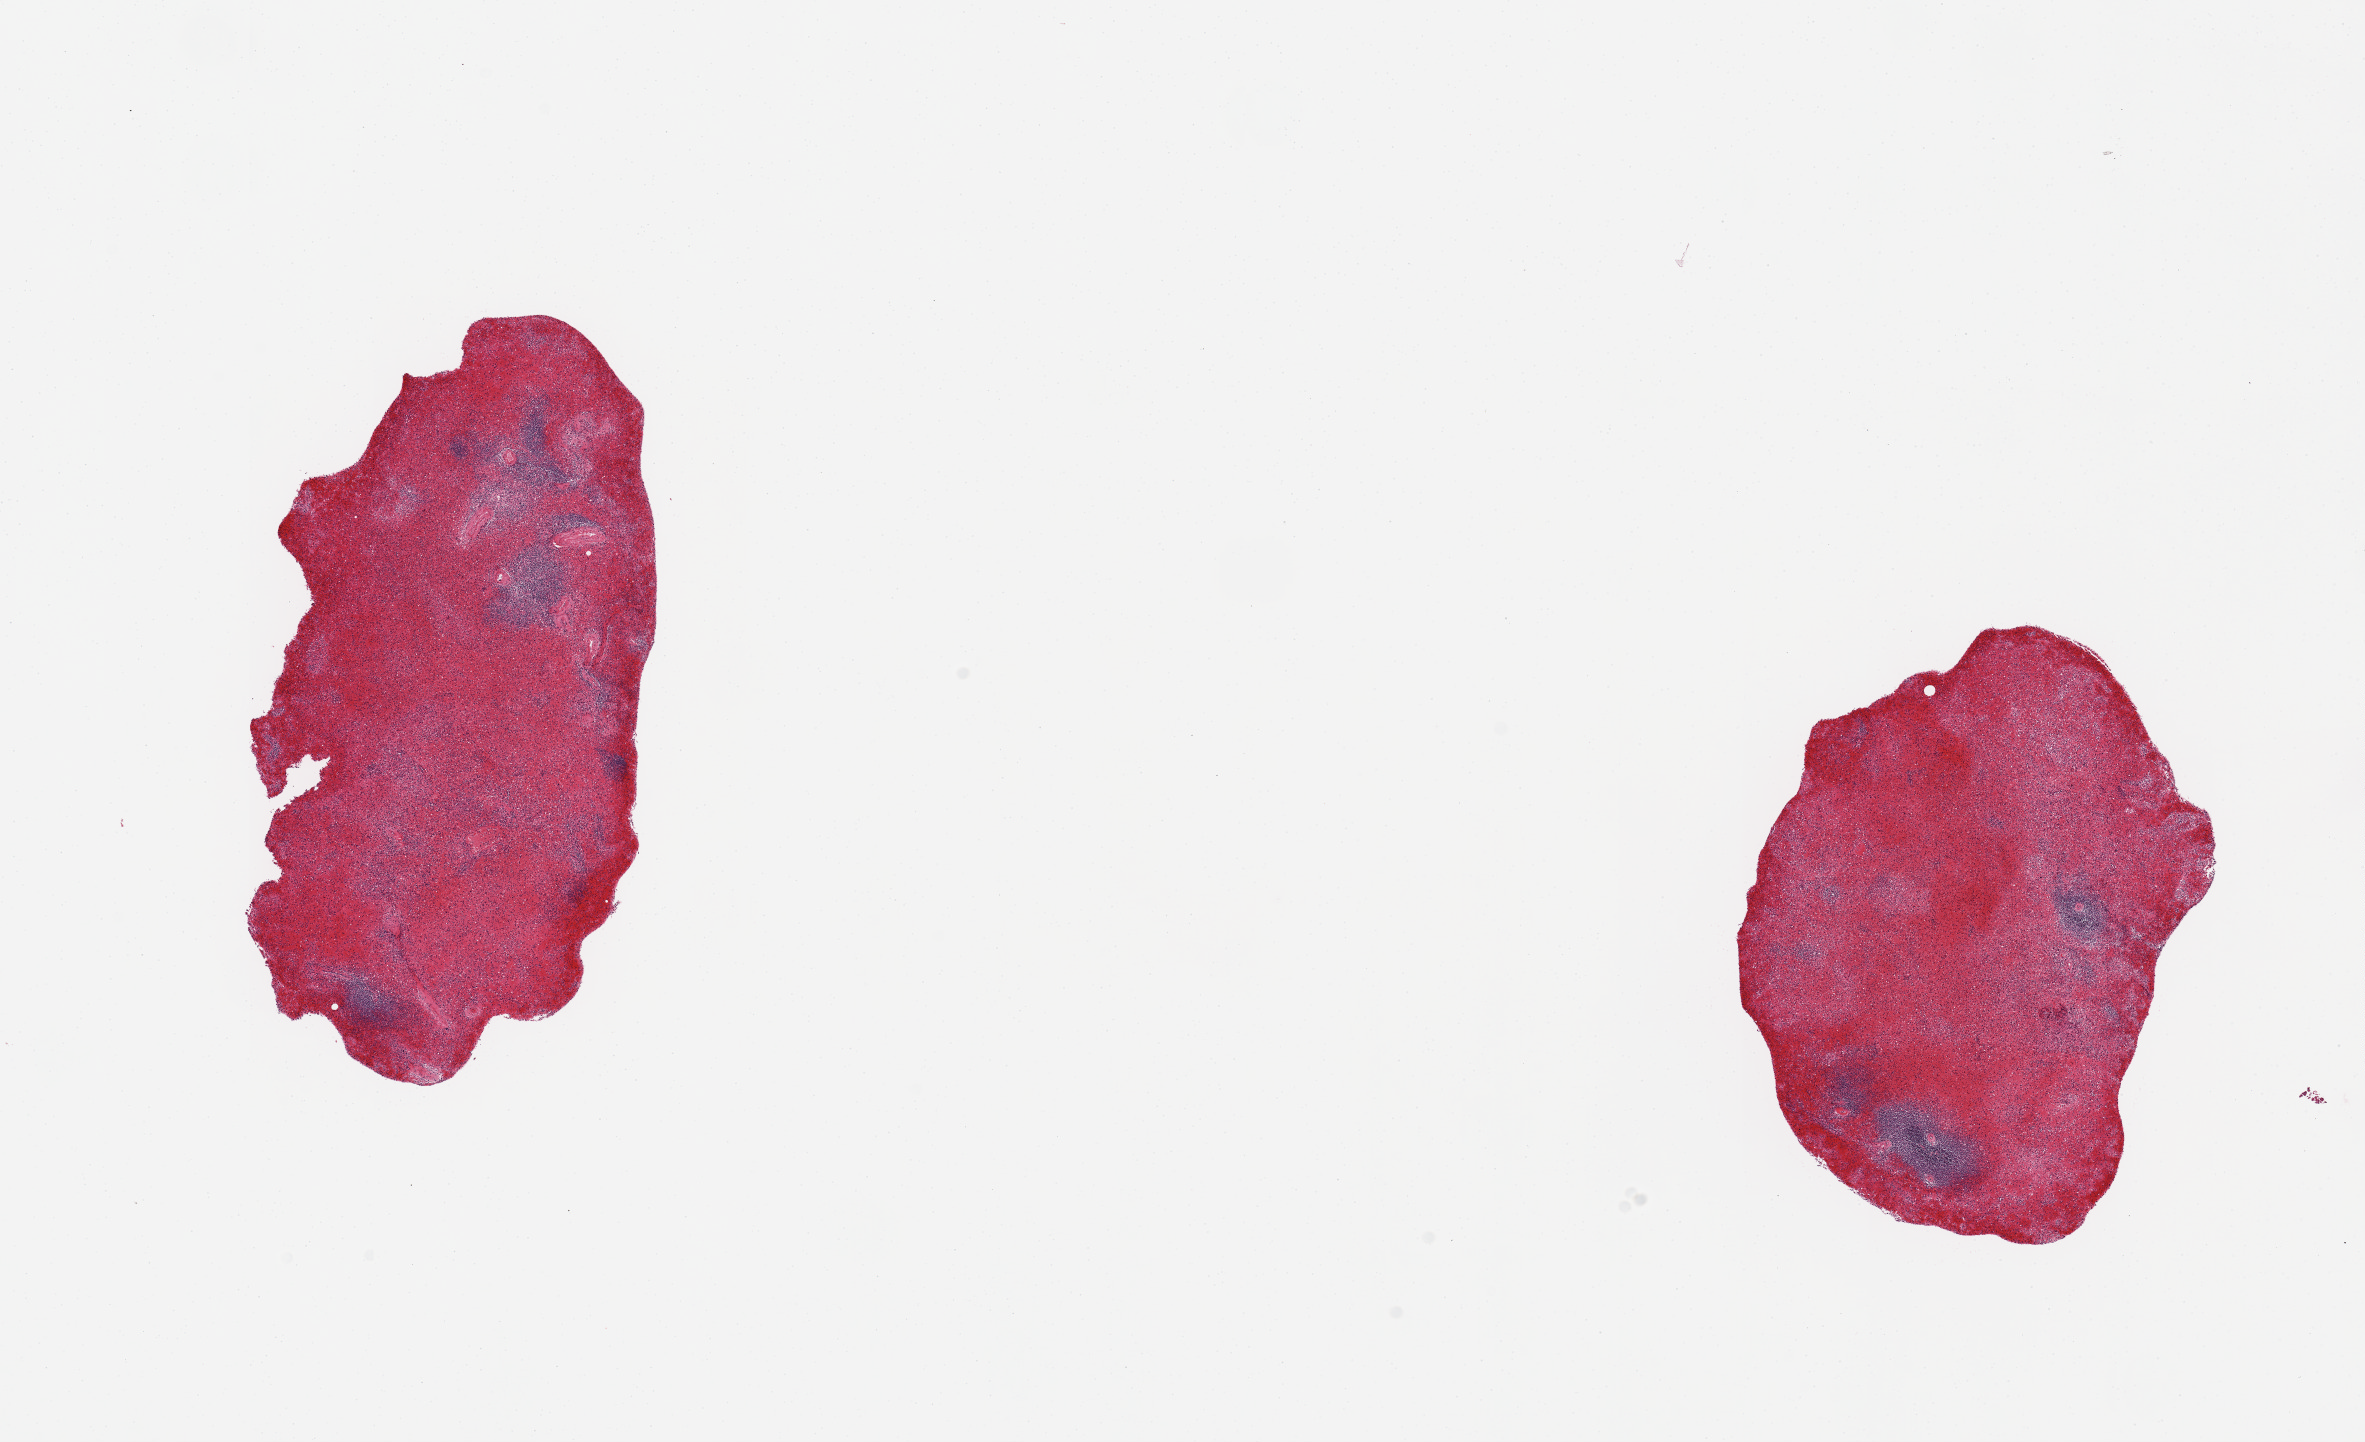
Haematoxylin and eosin whole-slide image — low-resolution overview of the scanned area, about 18.7 x 11.4 mm, PAXgene-fixed paraffin-embedded (PFPE) section, section of spleen (target tissue), donor tissue sample.
* reviewer comment on this tissue sample: 2 pieces; marked congestion